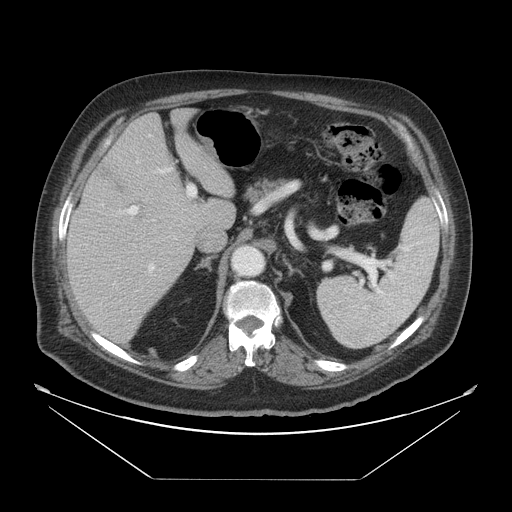
Contrast-enhanced abdominal CT, one axial slice; position 33 of 45 along the scan axis; reconstruction kernel STANDARD; intravenous contrast given; soft-tissue window (W 400 / L 40 HU); 5 mm slice thickness; 512 × 512 image matrix, field of view 463 × 463 mm. Male patient, age 87 years. Case-level facts recorded for this patient, not image findings: diagnosis: colorectal cancer liver metastases, imaged before liver resection; multiple liver metastases: no; largest metastasis: 4.5 cm; chemotherapy before resection: no.
Structures marked on this image (outlined manually by an expert reader):
- liver: bounding box [x1, y1, x2, y2] px = [66, 110, 237, 345]
- planned liver remnant (the part of the liver to remain after resection): [118, 111, 235, 193]
- portal vein (with intrahepatic branches): [119, 160, 196, 275]
- liver metastasis: [134, 203, 150, 228]
- liver metastasis: [95, 156, 145, 199]